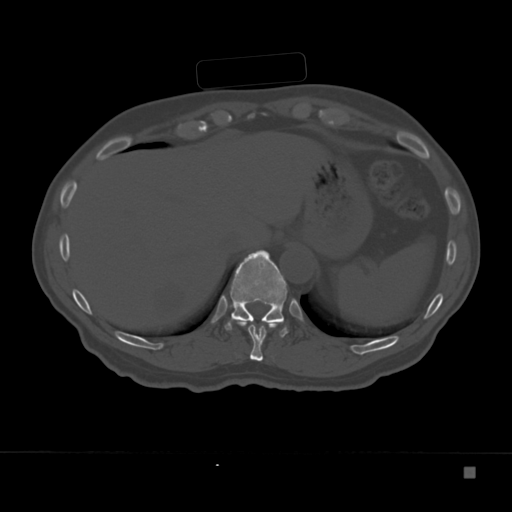
CT including the spine, one axial slice. Position 161 of 332 along the scan axis. Bone window (W 1800 / L 400 HU). 512 × 512 image matrix, field of view 389 × 389 mm. Male patient, age 72 years. From the clinical record (not read from this slice): primary cancer: skeletal.
Structures marked on this image (semi-automatically segmented with operator editing):
- T10 vertebra: box from (x=238, y=321) to (x=286, y=362) px
- T11 vertebra: (x=225, y=250)–(x=289, y=334)